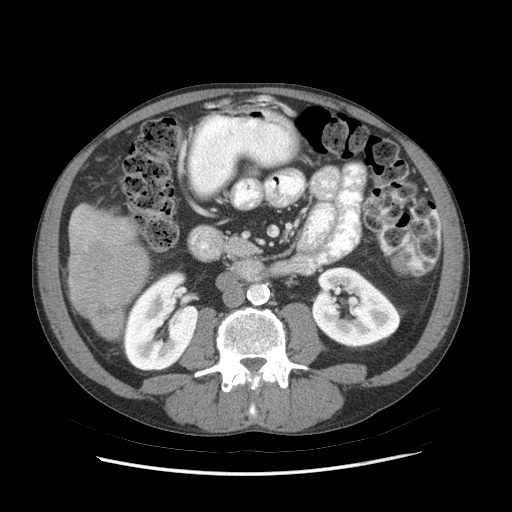
Contrast-enhanced abdominal CT (liver protocol), one axial slice; slice 18 of 89 in the series (ordered by position); 140 kVp; soft-tissue window (W 400 / L 40 HU); 512 × 512 image matrix, field of view 380 × 380 mm. From the clinical record (not read from this slice): diagnosis: hepatocellular carcinoma (patient treated with transarterial chemoembolisation; whether this scan precedes or follows treatment is not stated here); TNM stage (as recorded): Stage-IIIB; Child-Pugh class: A; tumour differentiation: moderately differentiated.
Annotated regions visible in this slice (semi-automatic segmentation, software-assisted and operator-edited):
- liver parenchyma outside the tumour (the mass and vessels are separate outlines, so this box may not span the whole liver): bounding box [x1, y1, x2, y2] px = [68, 204, 148, 339]
- mass: [69, 240, 147, 325]